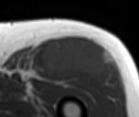
MRI of an extremity soft-tissue mass, one axial slice. Position 68 of 86 along the scan axis. MR volume resampled by the dataset authors to the PET/CT grid (not the native acquisition matrix). 139 × 117 image matrix, field of view 136 × 114 mm. Male patient. Case-level facts recorded for this patient, not image findings: histological type: extraskeletal osteosarcoma; grade: high; site of the primary tumour: thigh.
Structures marked on this image (expert contour drawn on MRI and transferred to this co-registered scan by the dataset authors):
- gross tumour volume (mass): bounding box [x1, y1, x2, y2] px = [40, 39, 108, 78]